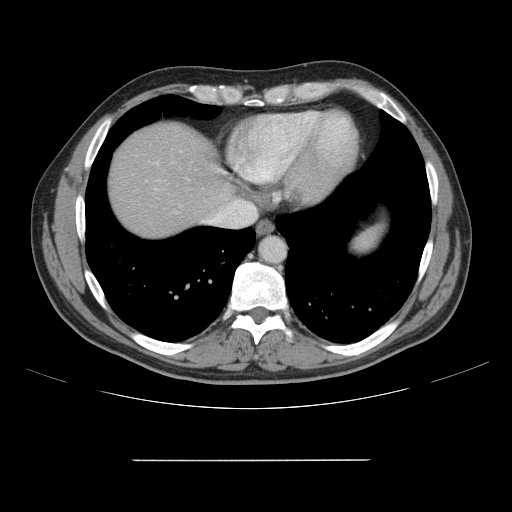
Contrast-enhanced abdominal CT, one axial slice. Position 141 of 164 along the scan axis. Intravenous contrast given. Soft-tissue window (W 400 / L 40 HU). 2.5 mm slice thickness. 512 × 512 image matrix, field of view 404 × 404 mm. Male patient, age 54 years. Case-level facts recorded for this patient, not image findings: diagnosis: colorectal cancer liver metastases, imaged before liver resection; multiple liver metastases: yes; largest metastasis: 1 cm; chemotherapy before resection: yes.
Annotated regions visible in this slice (outlined manually by an expert reader):
- hepatic veins: box from (x=204, y=200) to (x=258, y=227) px
- liver: (x=108, y=122)–(x=234, y=238)
- planned liver remnant (the part of the liver to remain after resection): (x=108, y=122)–(x=232, y=238)